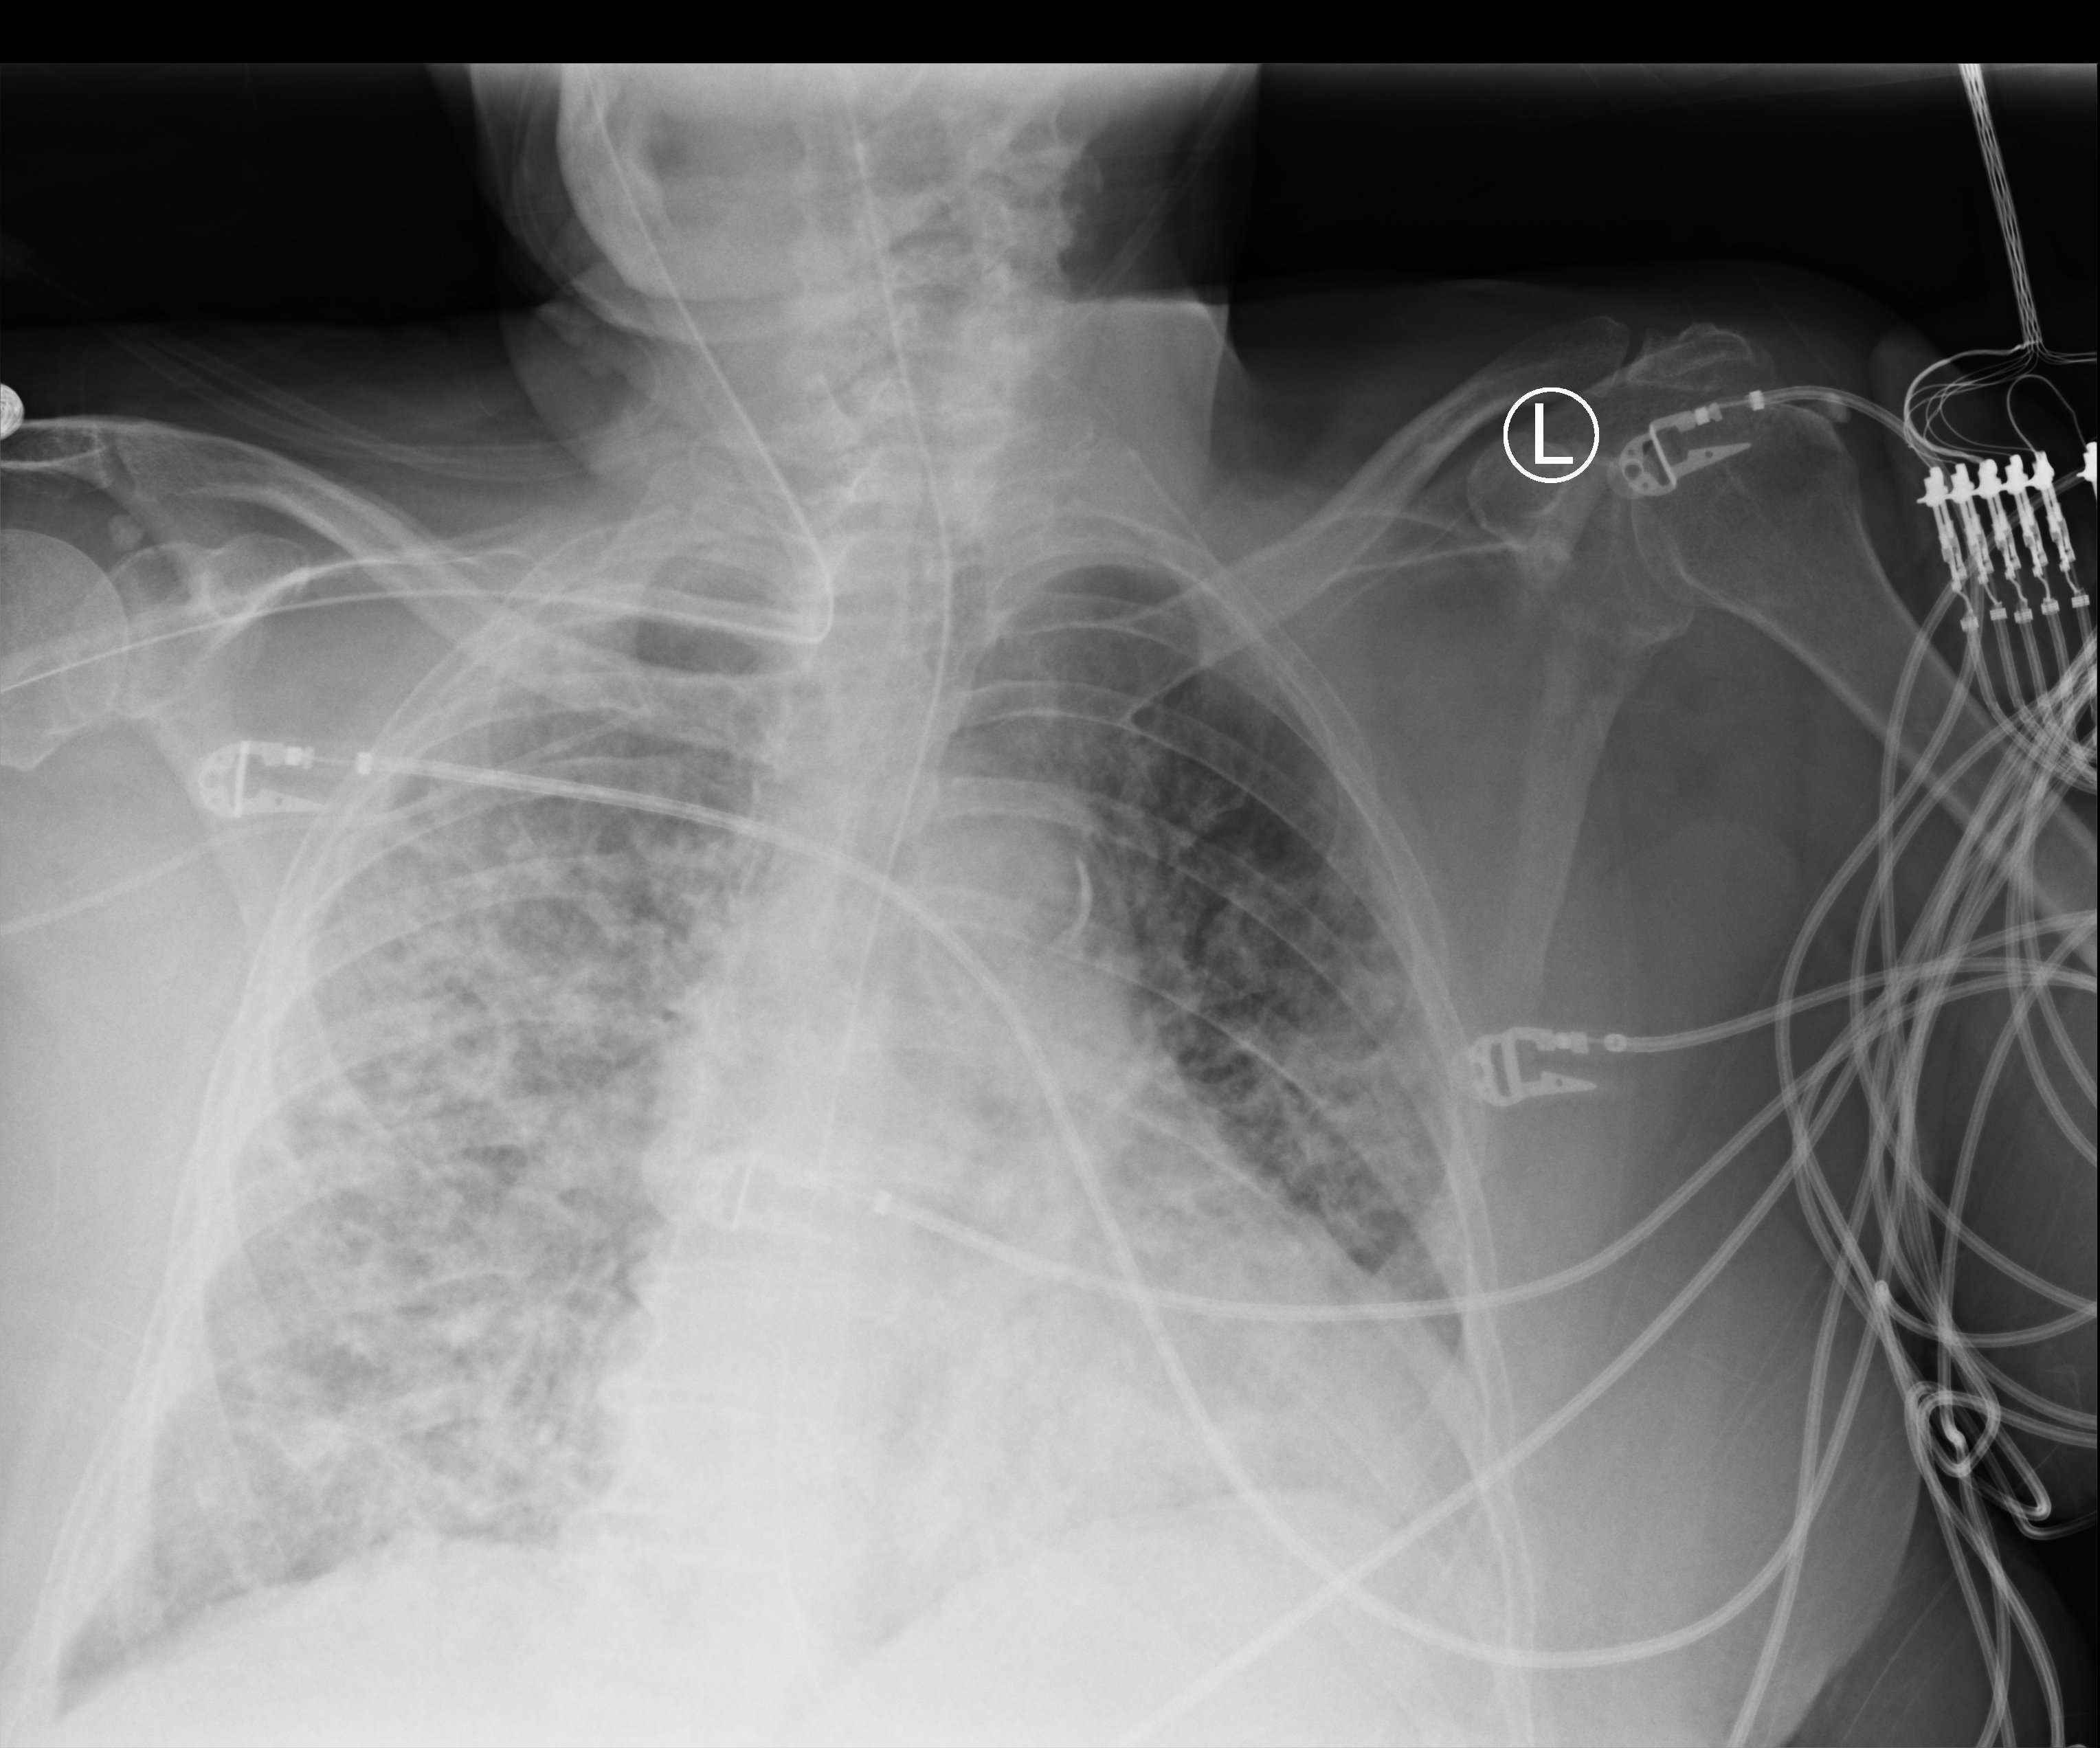
Portable chest radiograph. Female patient hospitalised with COVID-19, age 75–90 years.
Hospital-stay facts (about this admission, not read from this image; timing relative to this image not recorded):
- admitted to intensive care during this hospital stay: yes
- chronic kidney disease (admission record): no